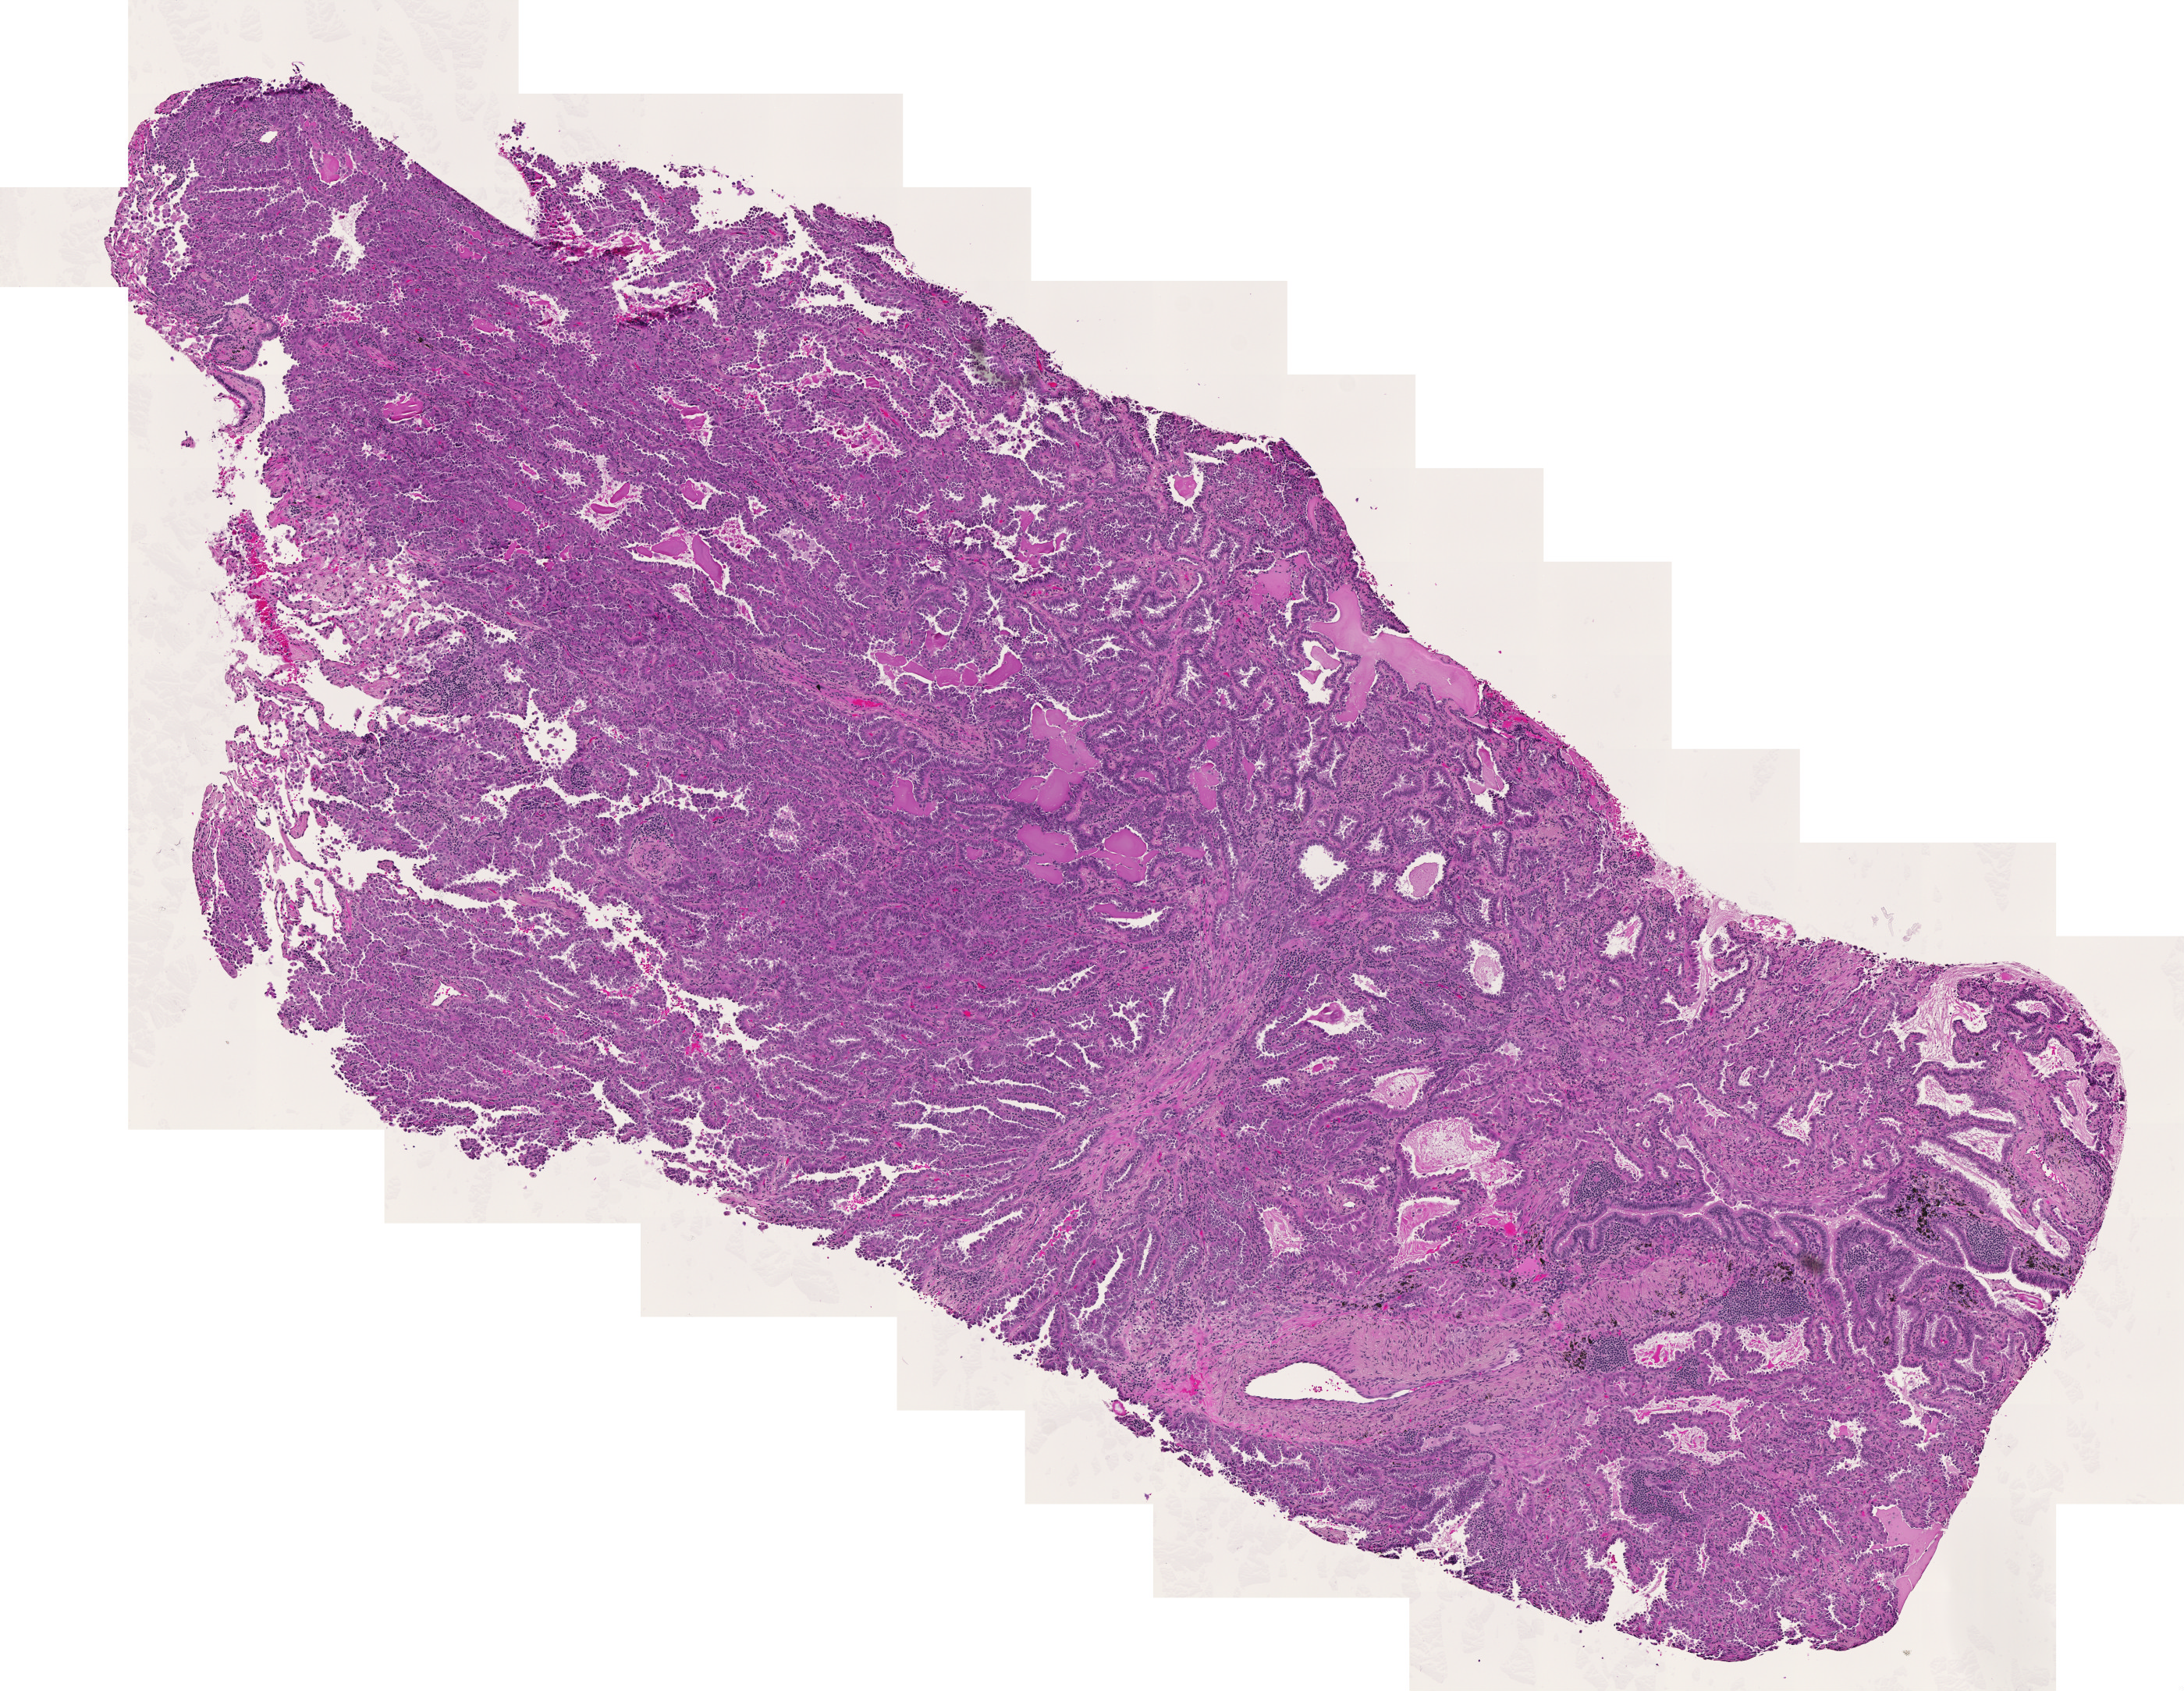
Whole-slide histology image, Hematoxylin and eosin (H&E) stained — whole scanned area (about 7.2 x 5.6 mm) shown as a low-resolution overview, tumour tissue sample, lung. 73-year-old male patient. Histologic grade: G1 (well differentiated).
• AJCC pathologic stage: IA
• histologic diagnosis: Adenocarcinoma, NOS